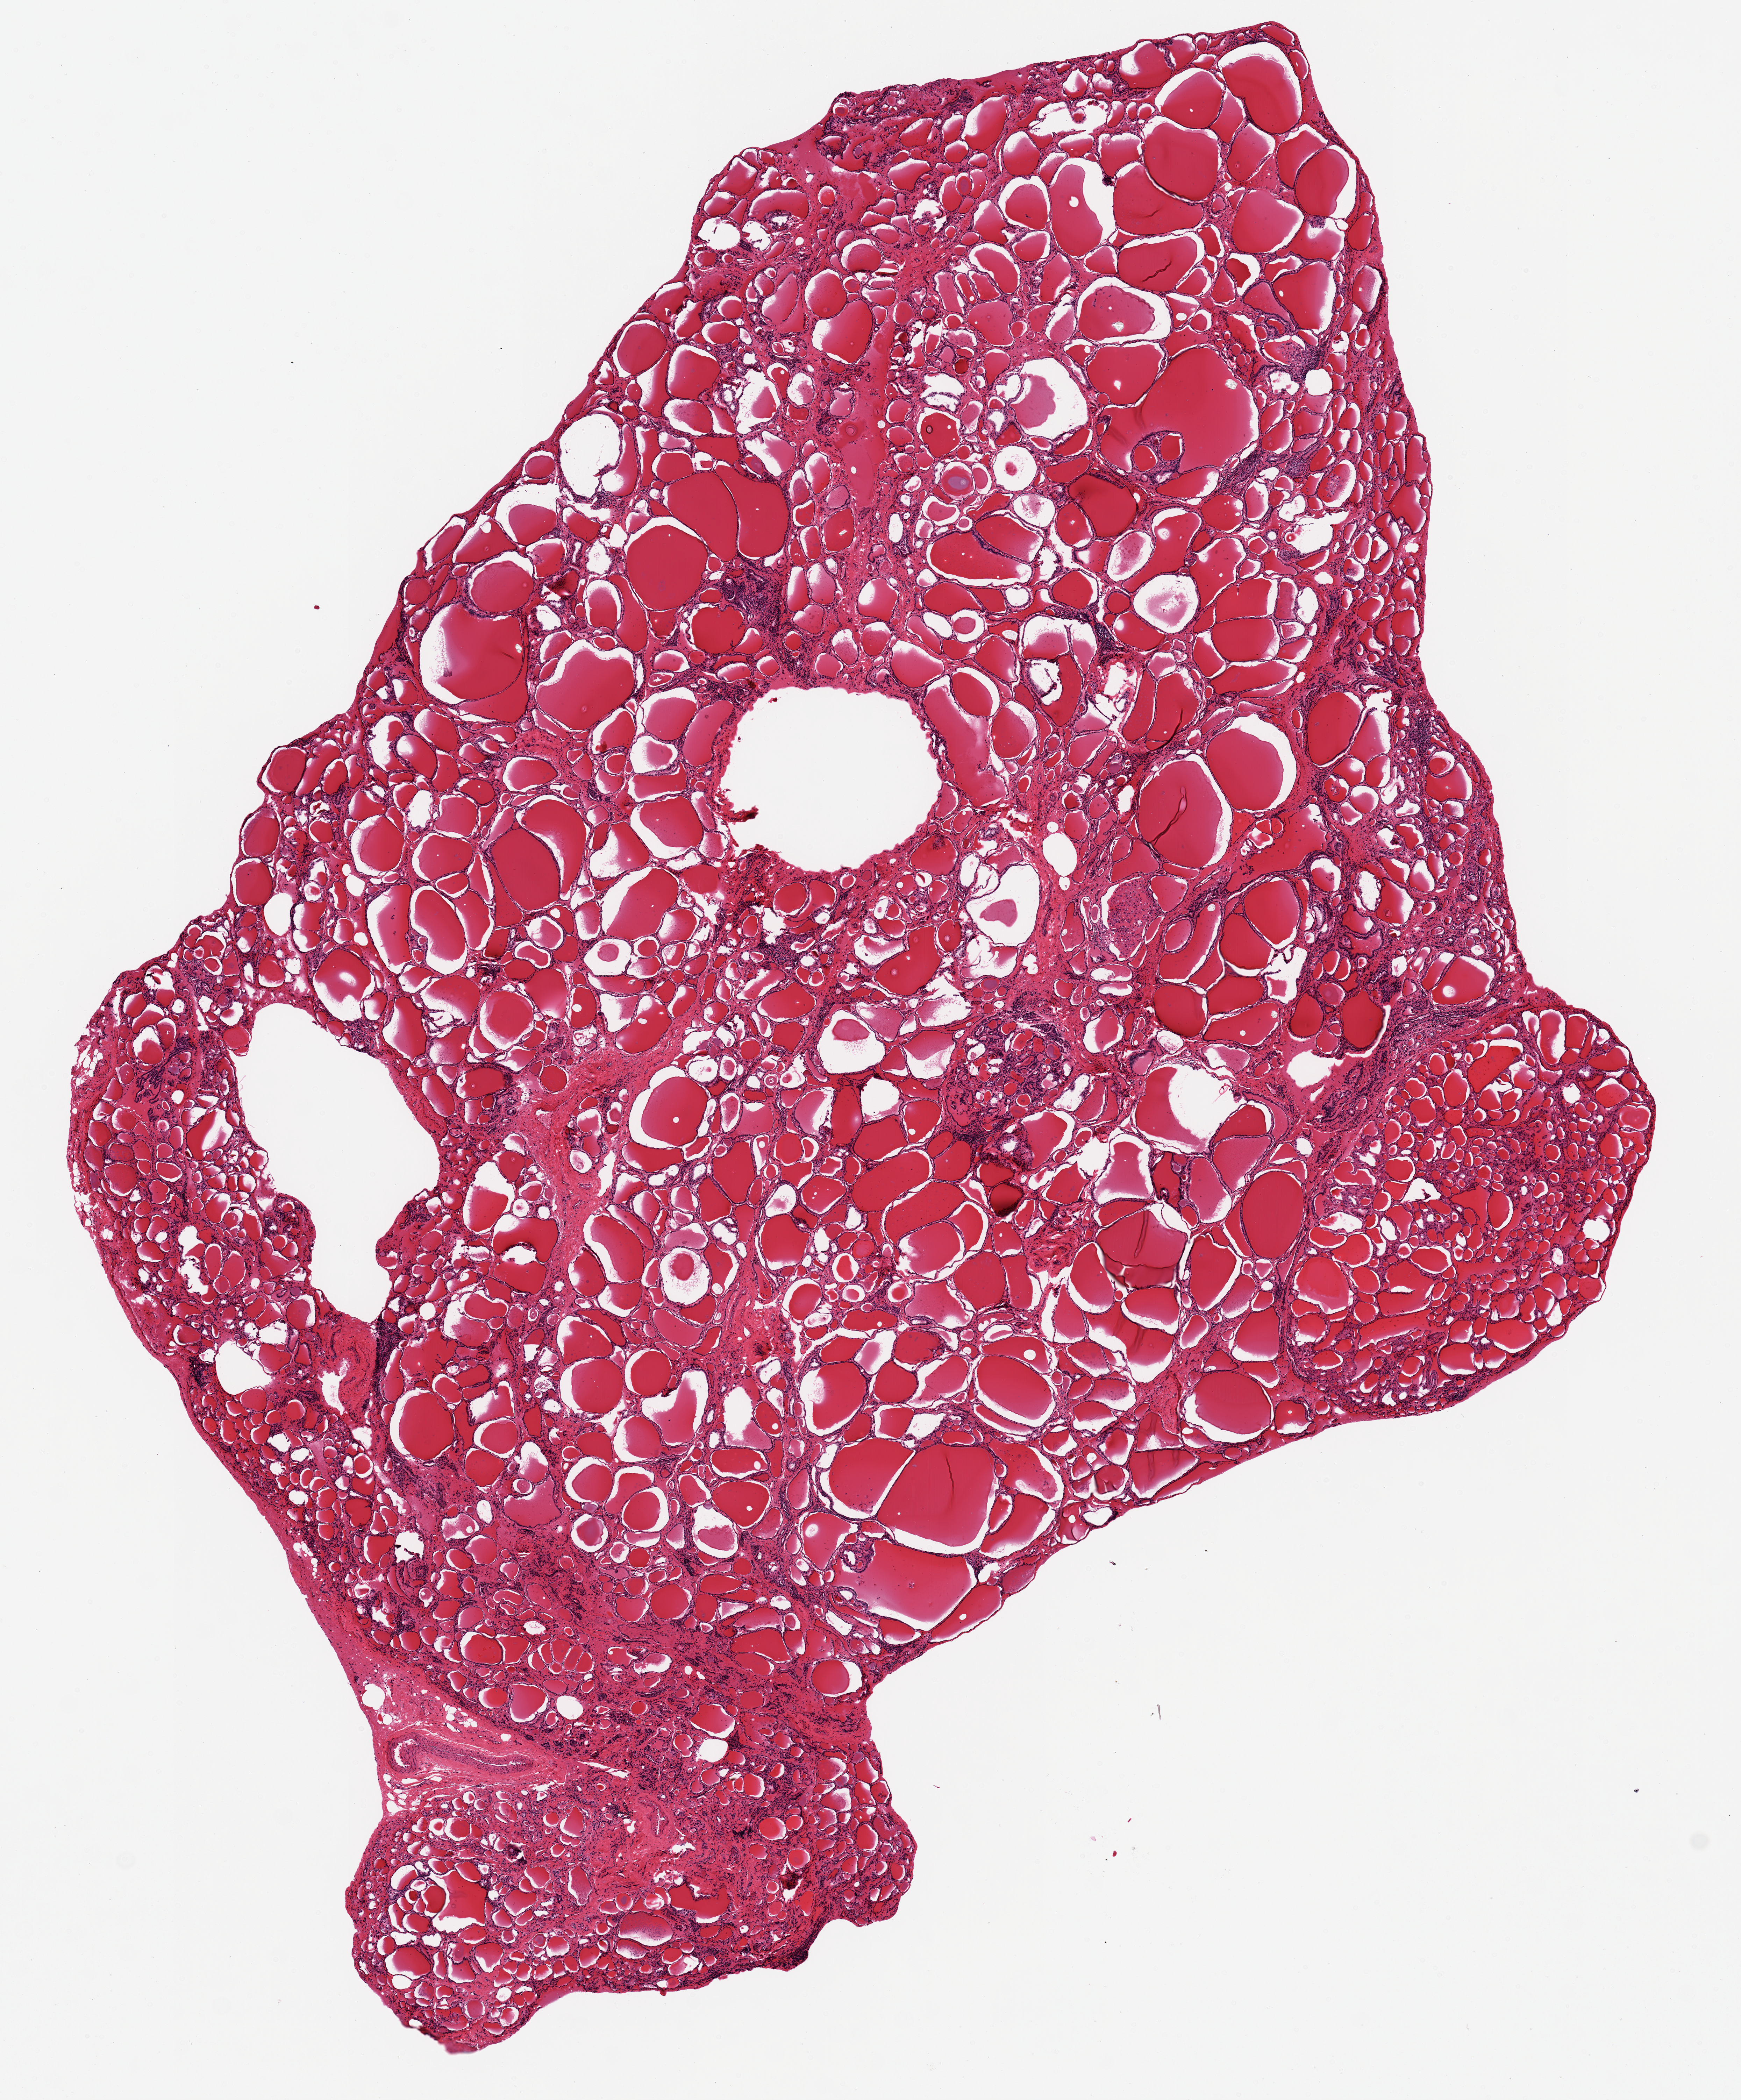
Digitized H&E-stained section, whole scanned area (about 9.8 x 11.9 mm) shown as a low-resolution overview; PAXgene-fixed, paraffin-embedded tissue; sampled site (target tissue): thyroid; donor tissue sample.
- pathologist's review note for this sample: 2 x 1 mm adenomatoid nodule, peripheral